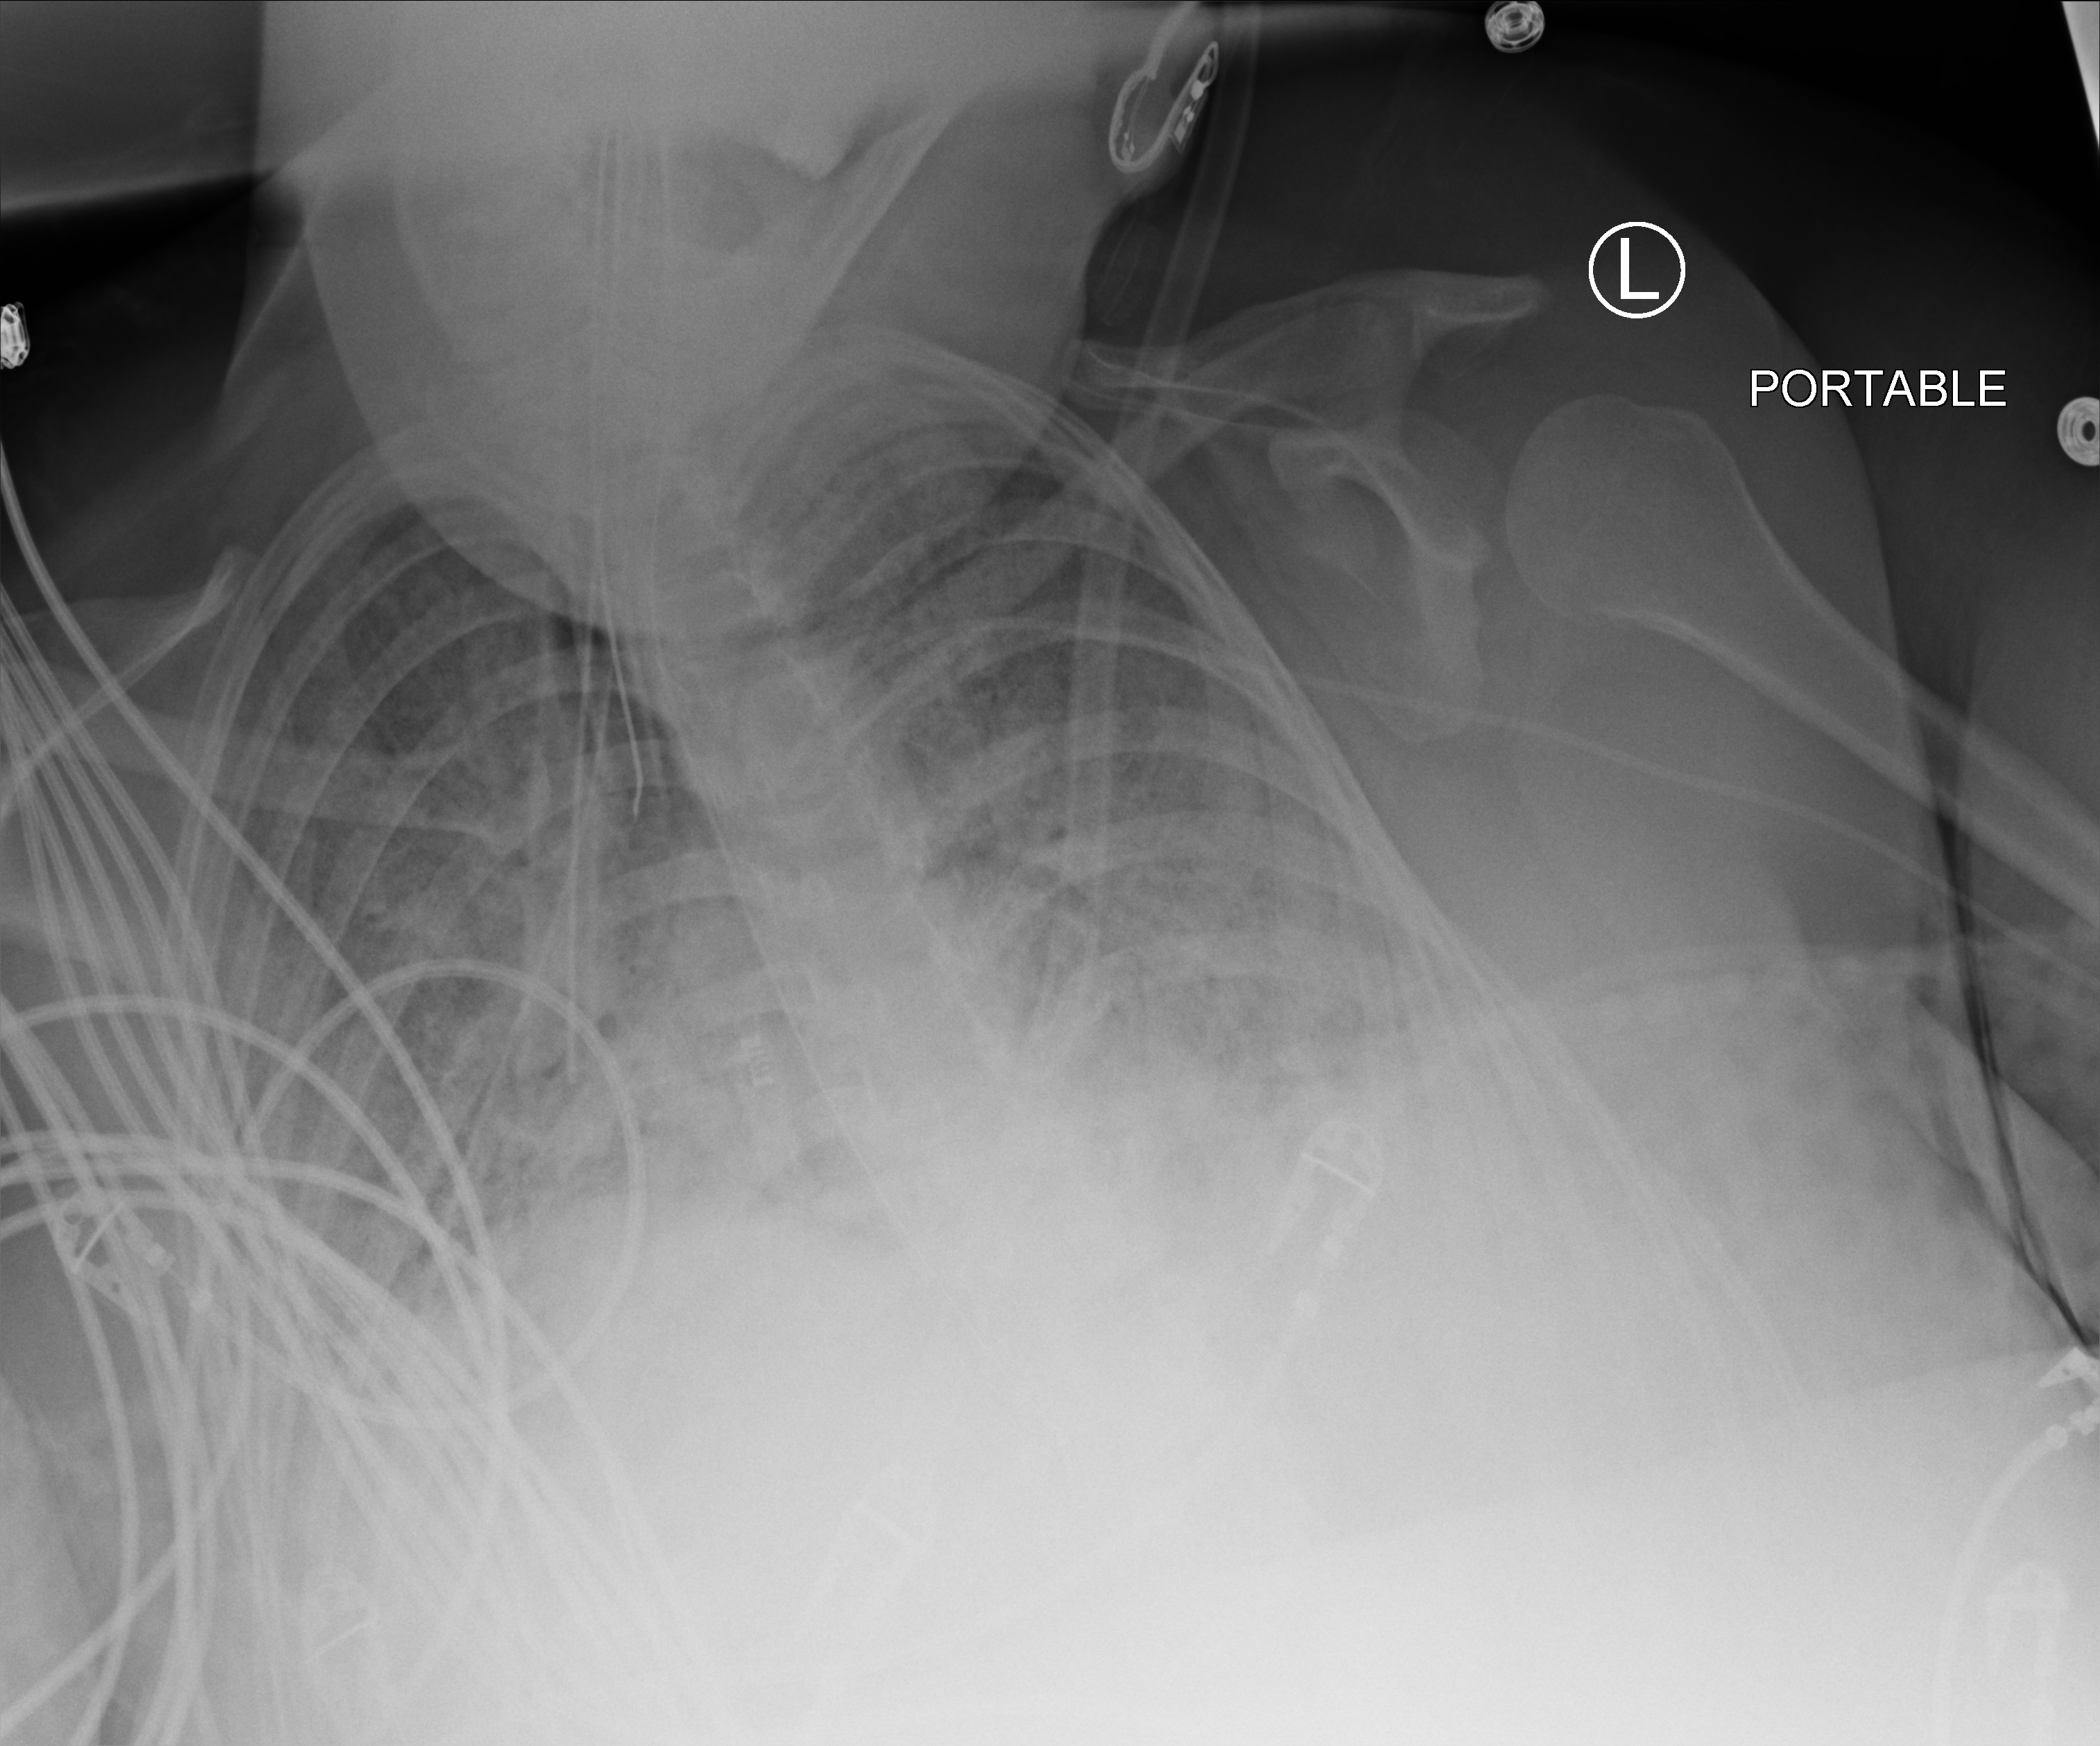
Chest X-ray (portable), anteroposterior (AP) projection. Female patient hospitalised with COVID-19, age 18–59 years.
From the hospital-stay record, not from the radiograph (when in the stay this image was taken is not recorded): diabetes (admission record): no.